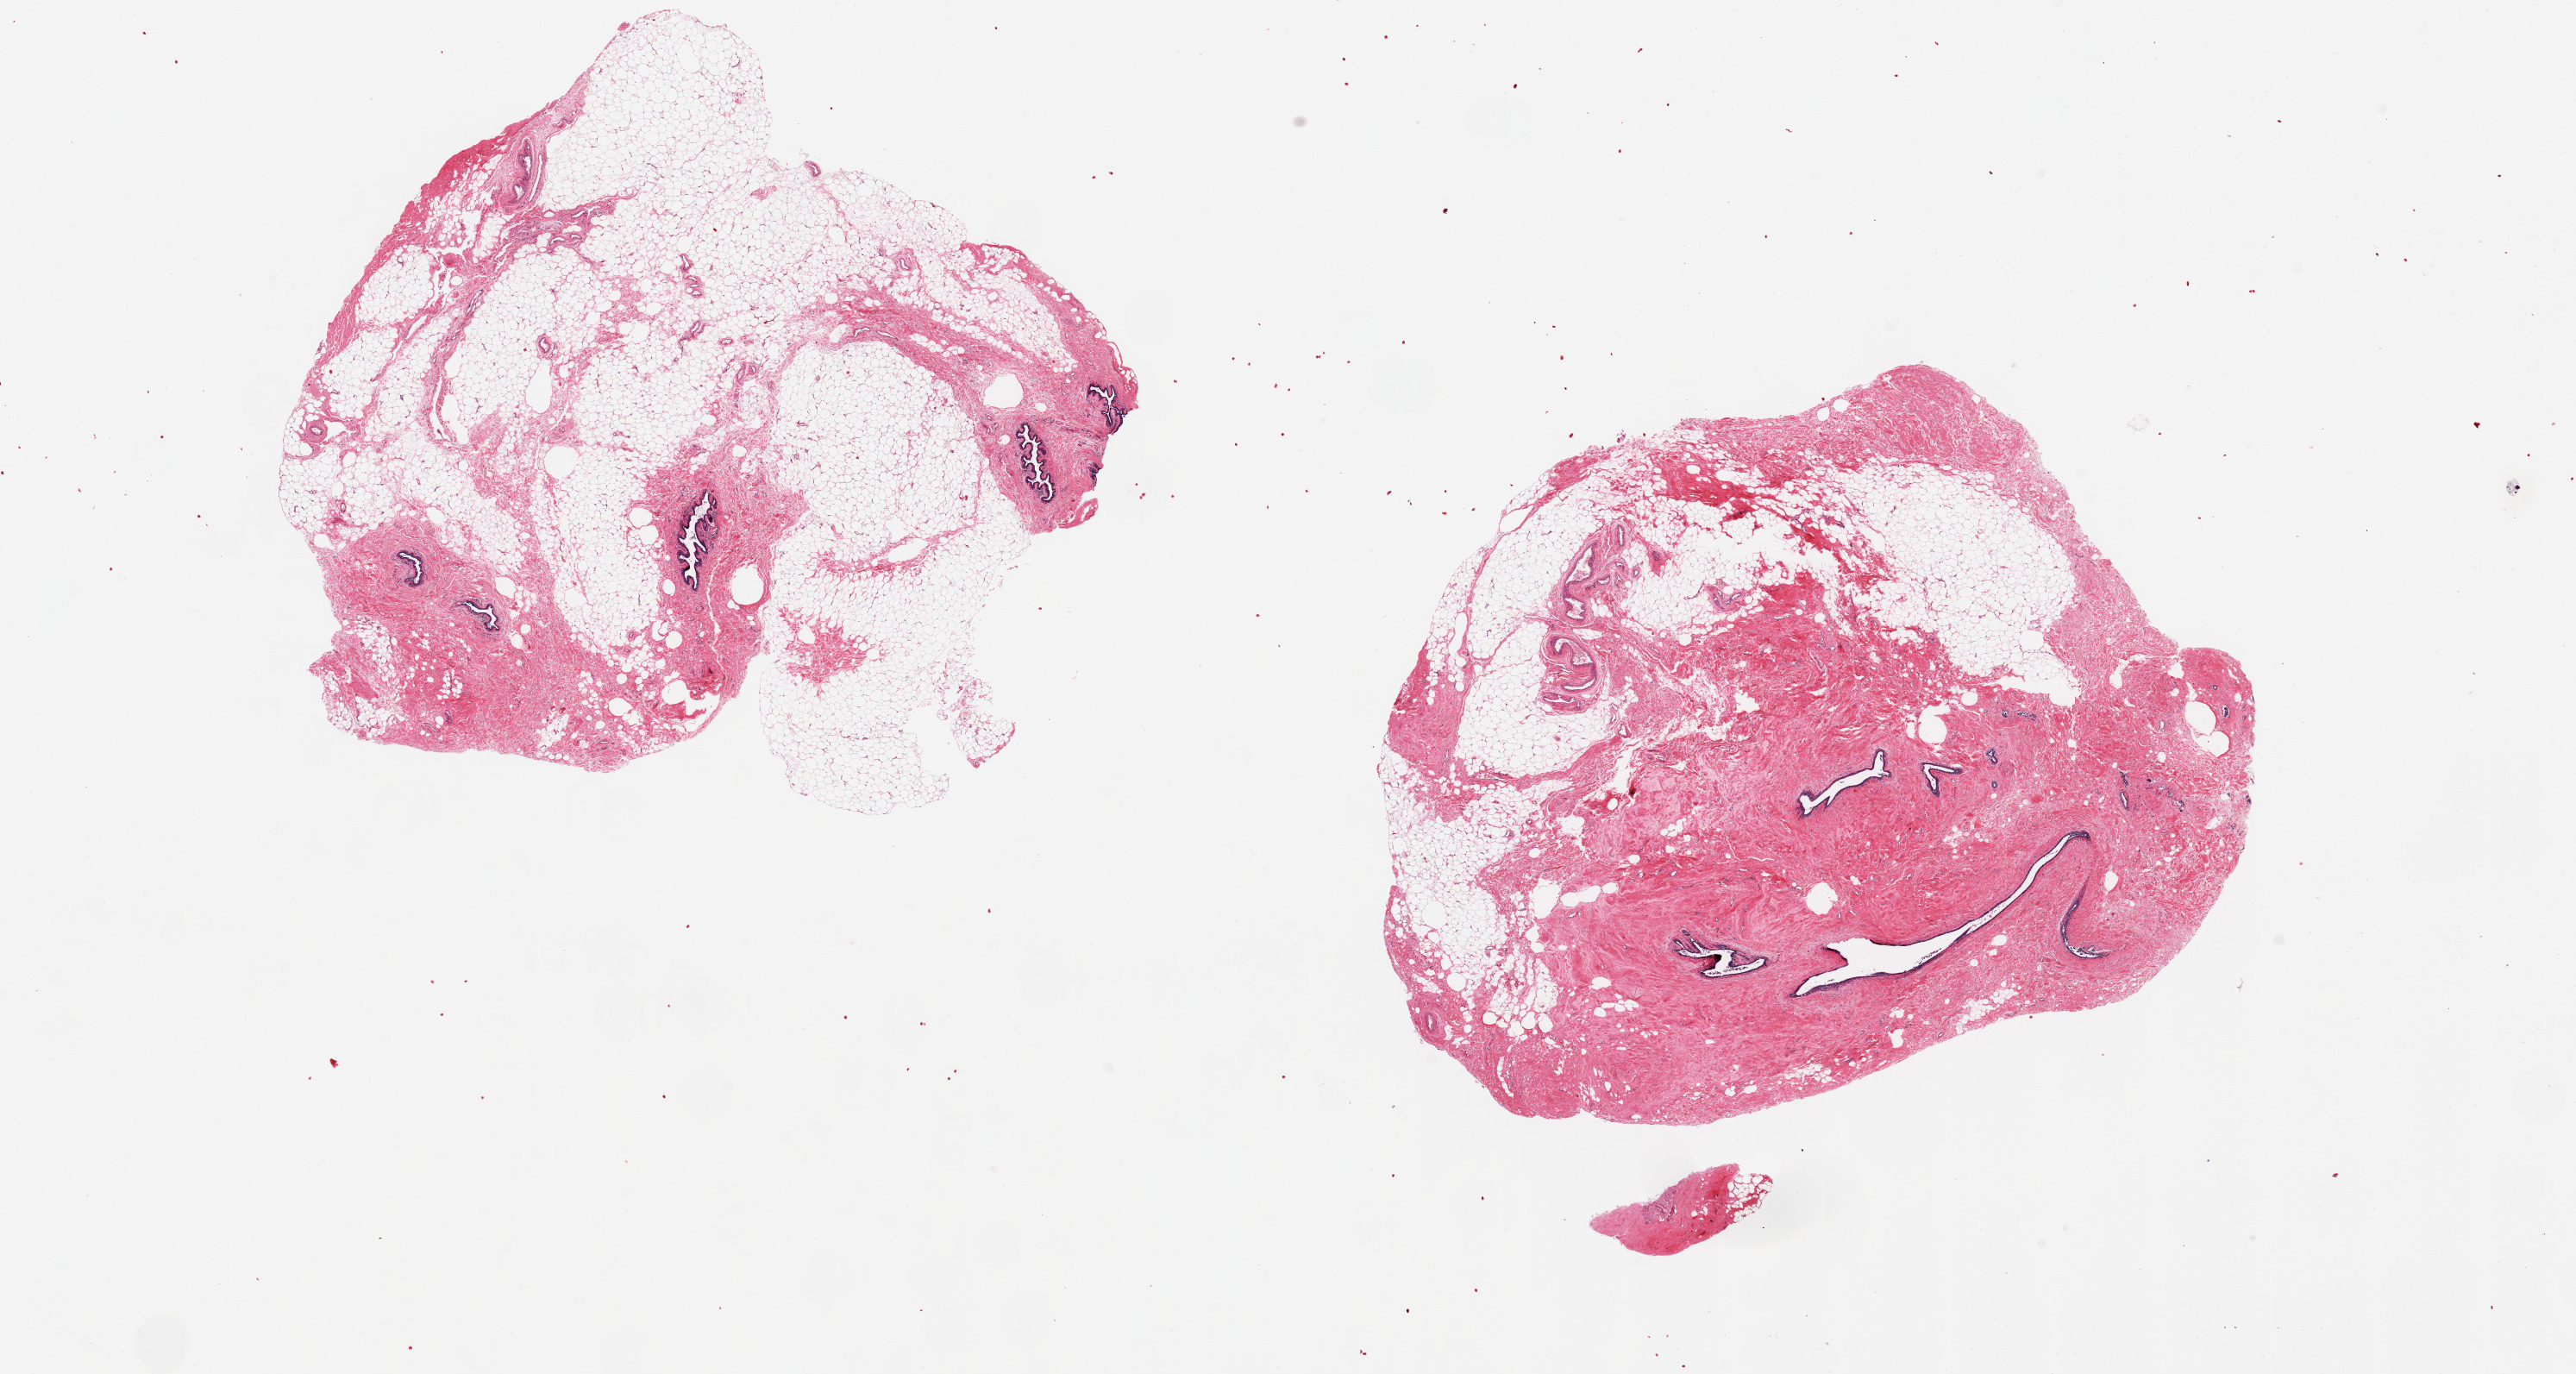
Haematoxylin and eosin whole-slide image, shown as a low-resolution overview of the whole scanned area (about 23.6 x 12.6 mm, slide scanned at 20x); PAXgene-fixed, paraffin-embedded tissue; sampled site (target tissue): breast; donor tissue sample. Female donor.
• review note (as recorded): 2 pieces, 8x6 & 7x7 mm; atrophic, ducts no lobules; 40 & 60% adipose